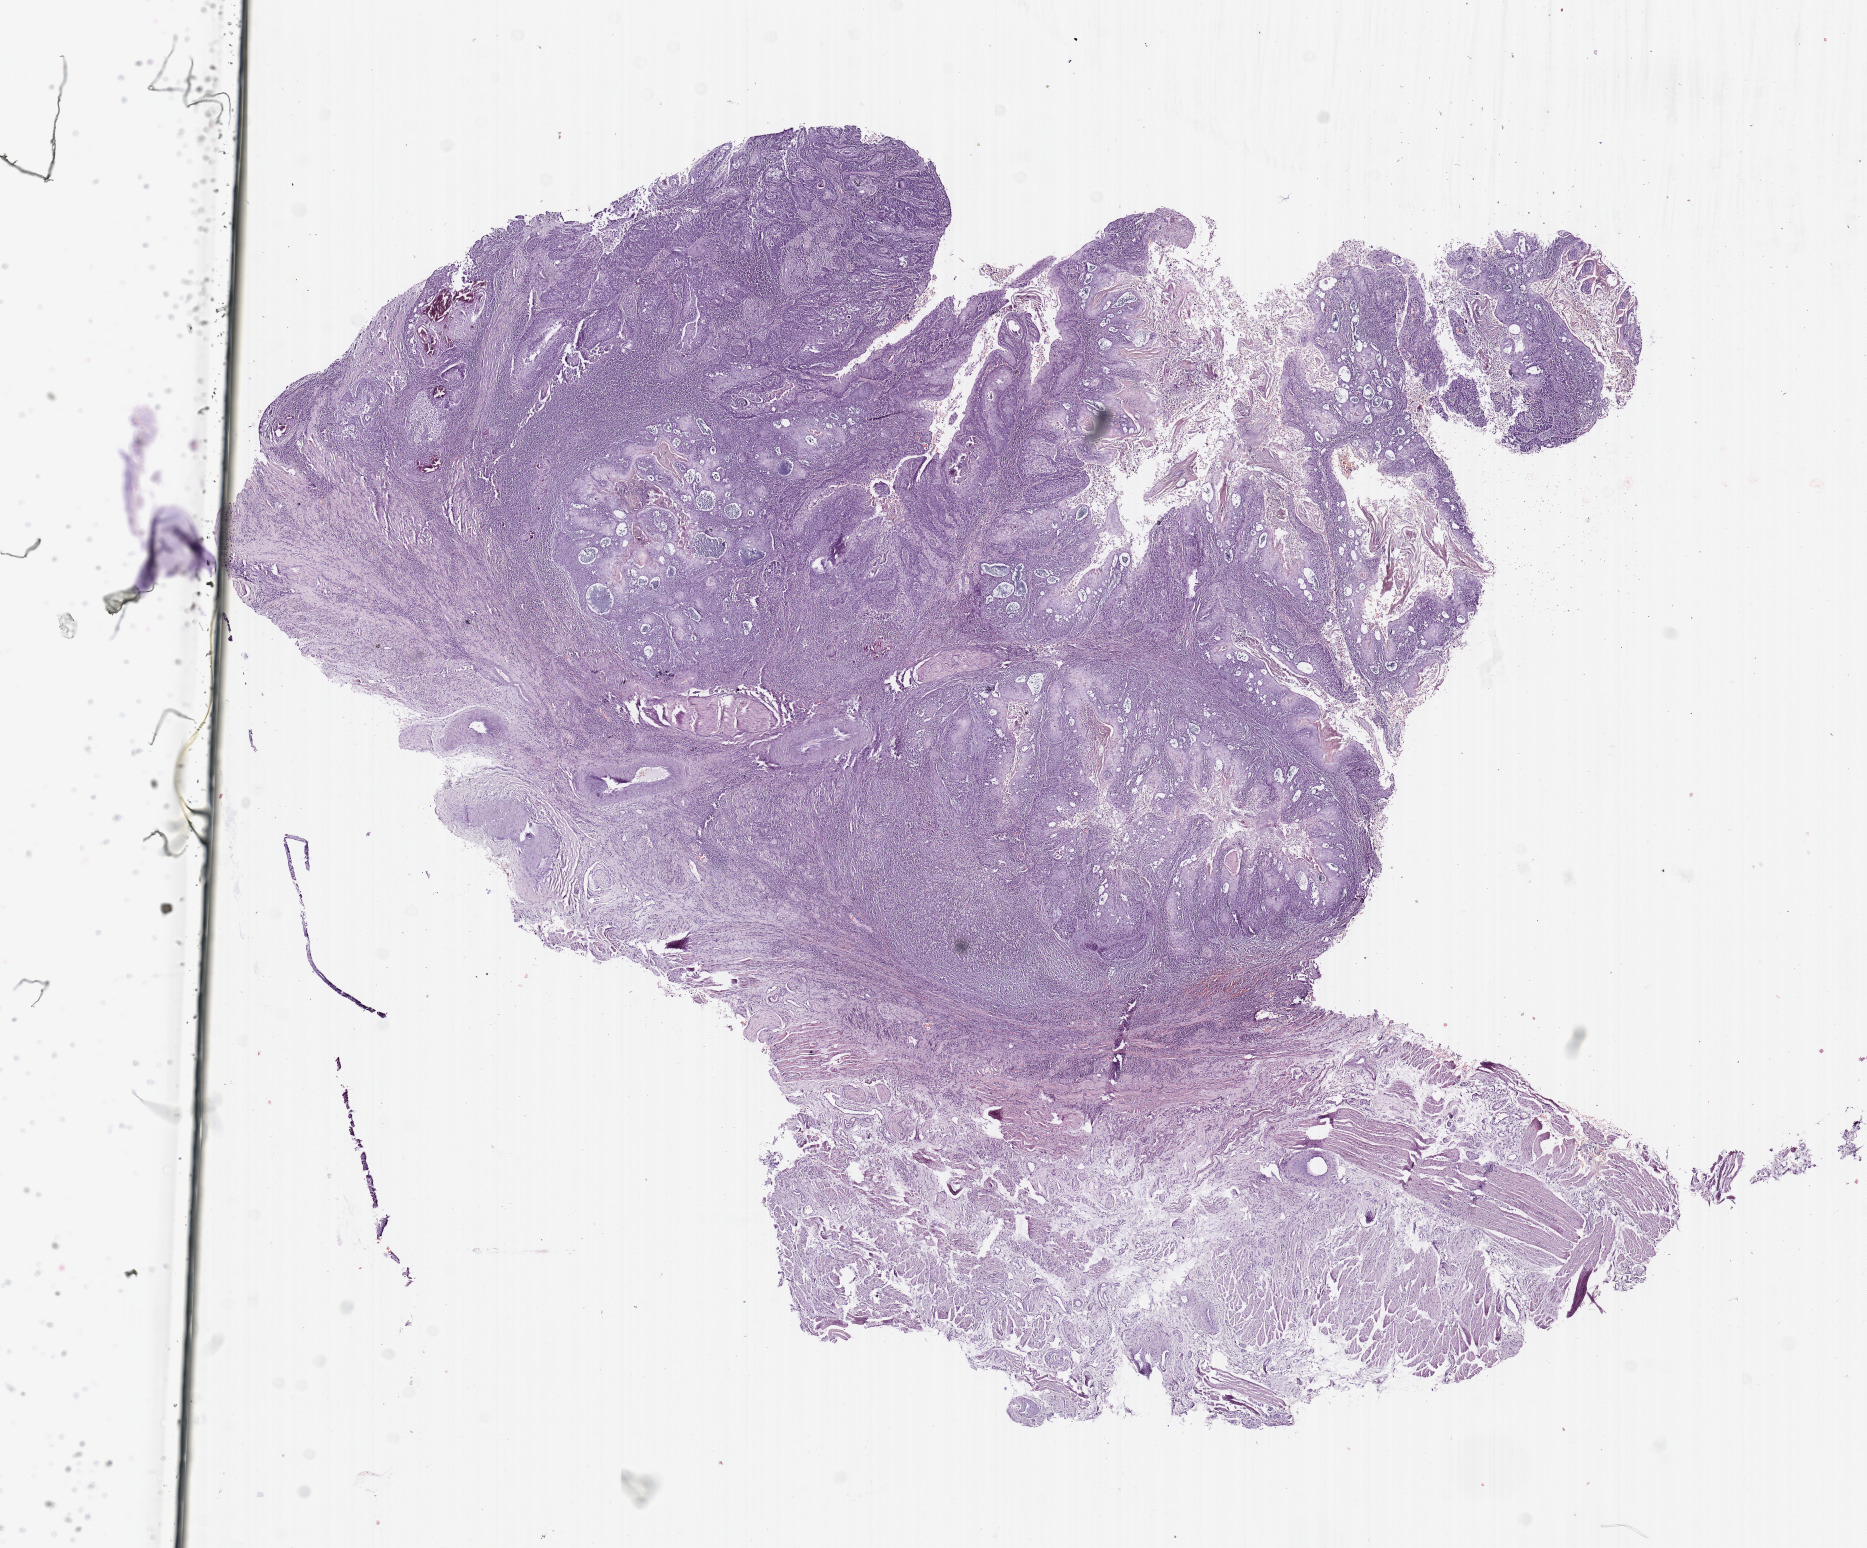
Whole-slide histology image, Hematoxylin and eosin (H&E) stained, shown as a low-resolution overview of the whole scanned area (about 14.8 x 12.2 mm, slide scanned at 20x); head and neck, tissue type not recorded. Patient: male, age 59 years.
• patient diagnosis: Squamous cell carcinoma, NOS (tongue, NOS)